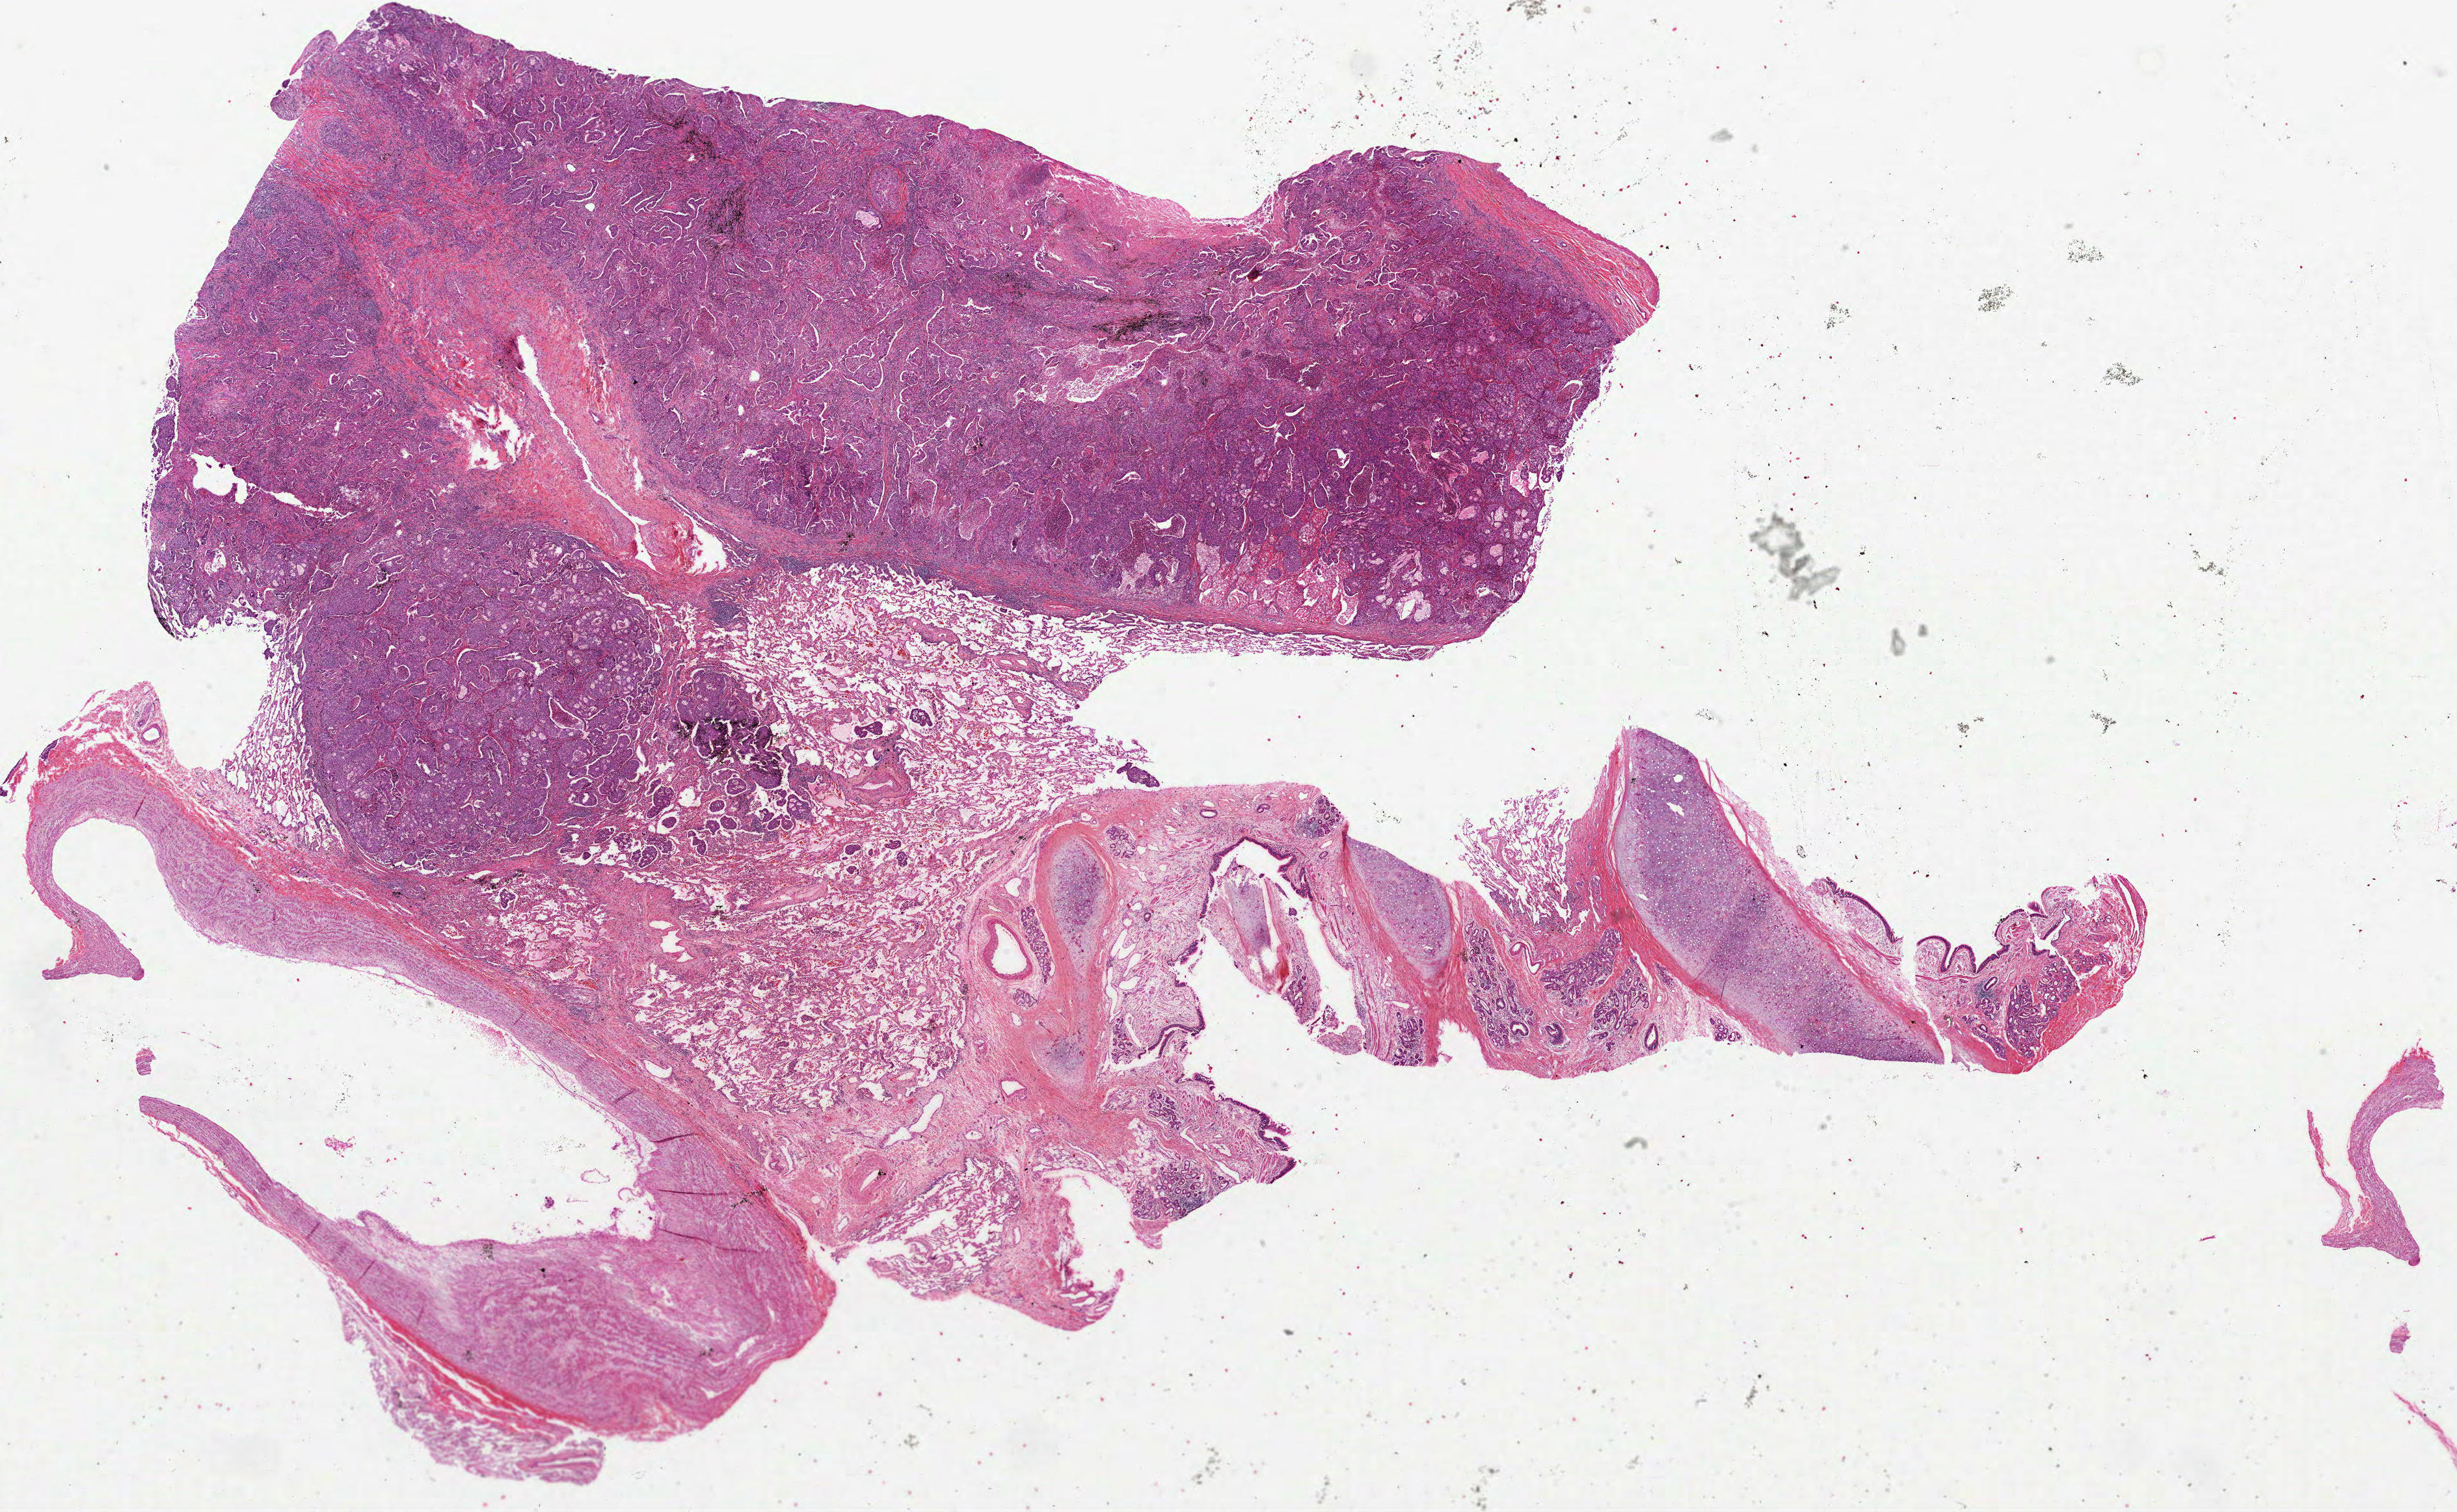
Whole-slide histology image, H&E — low-resolution overview of the scanned area, about 30.5 x 18.7 mm (acquisition: 40x scan). Formalin-fixed paraffin-embedded (FFPE) diagnostic section. Primary tumour sample from the lung. Male patient; age at initial diagnosis 77 years.
Histologic diagnosis: Adenocarcinoma, NOS (upper lobe, lung). AJCC pathologic stage: IIIA (4th edition).